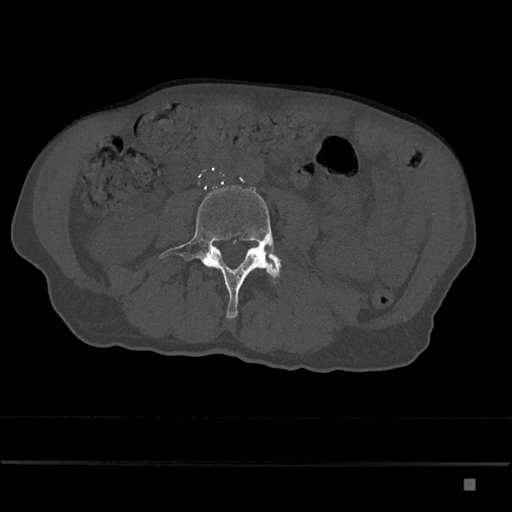
CT including the spine, one axial slice. Position 341 of 797 along the scan axis. Reconstruction kernel Br40s/3. Bone window (W 1800 / L 400 HU). 0.5 mm slice thickness. 512 × 512 image matrix, field of view 390 × 390 mm. Male patient, age 72 years. Case-level facts recorded for this patient, not image findings: primary cancer: prostate.
Outlined on this slice (semi-automatic segmentation, software-assisted and operator-edited):
- L4 vertebra: box from (x=159, y=185) to (x=280, y=319) px
- L5 vertebra: (x=270, y=255)–(x=281, y=270)